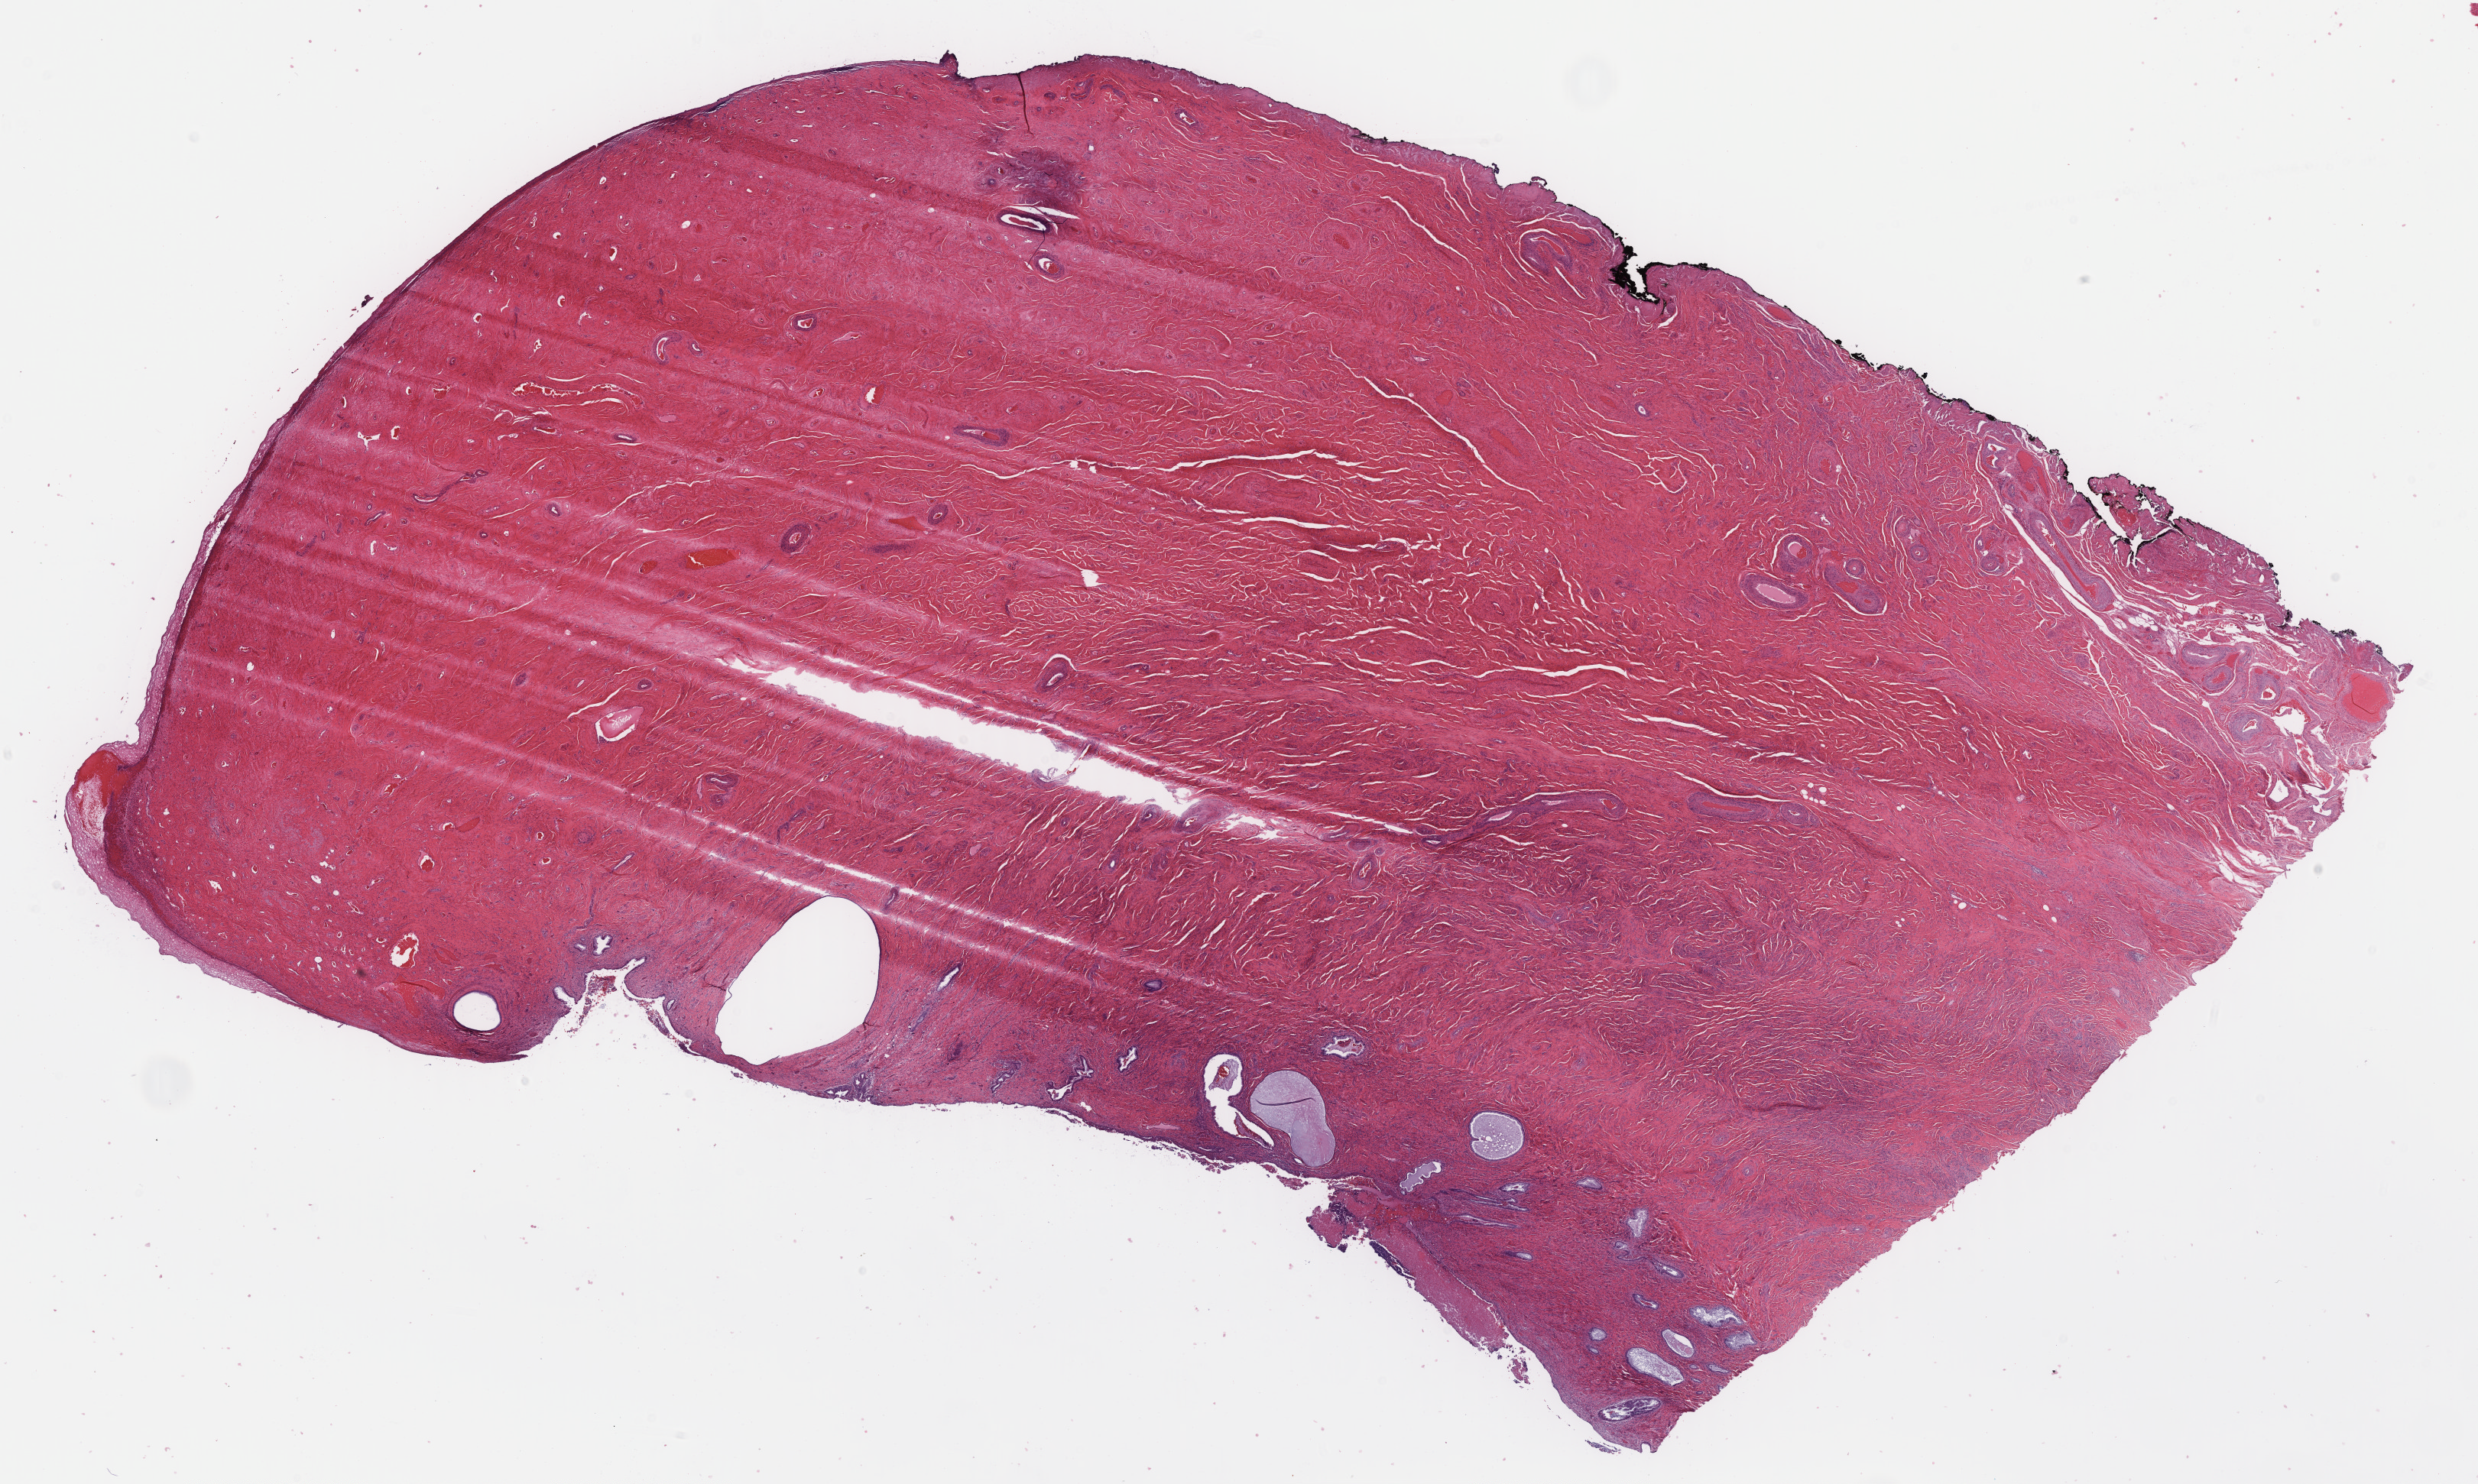
Whole-slide image, hematoxylin and eosin (H&E) stain, a low-resolution overview of the entire scanned area, about 25.7 x 15.4 mm, frozen section, specimen: normal-tissue sample (non-tumor) from a patient with carcinoma, undifferentiated, NOS, site: body of uterus. Patient sex: female. Pathologist review of this section (percent, as recorded): tumor cells 0%, tumor nuclei 0%, stromal cells 96%, necrosis 0%, normal cells 4%. Infiltration values recorded for this section: lymphocyte infiltration 1%, monocyte infiltration 1%, neutrophil infiltration 0%.
This section: non-tumor tissue sample; the patient's diagnosis is given above. Section: top of the tissue portion.